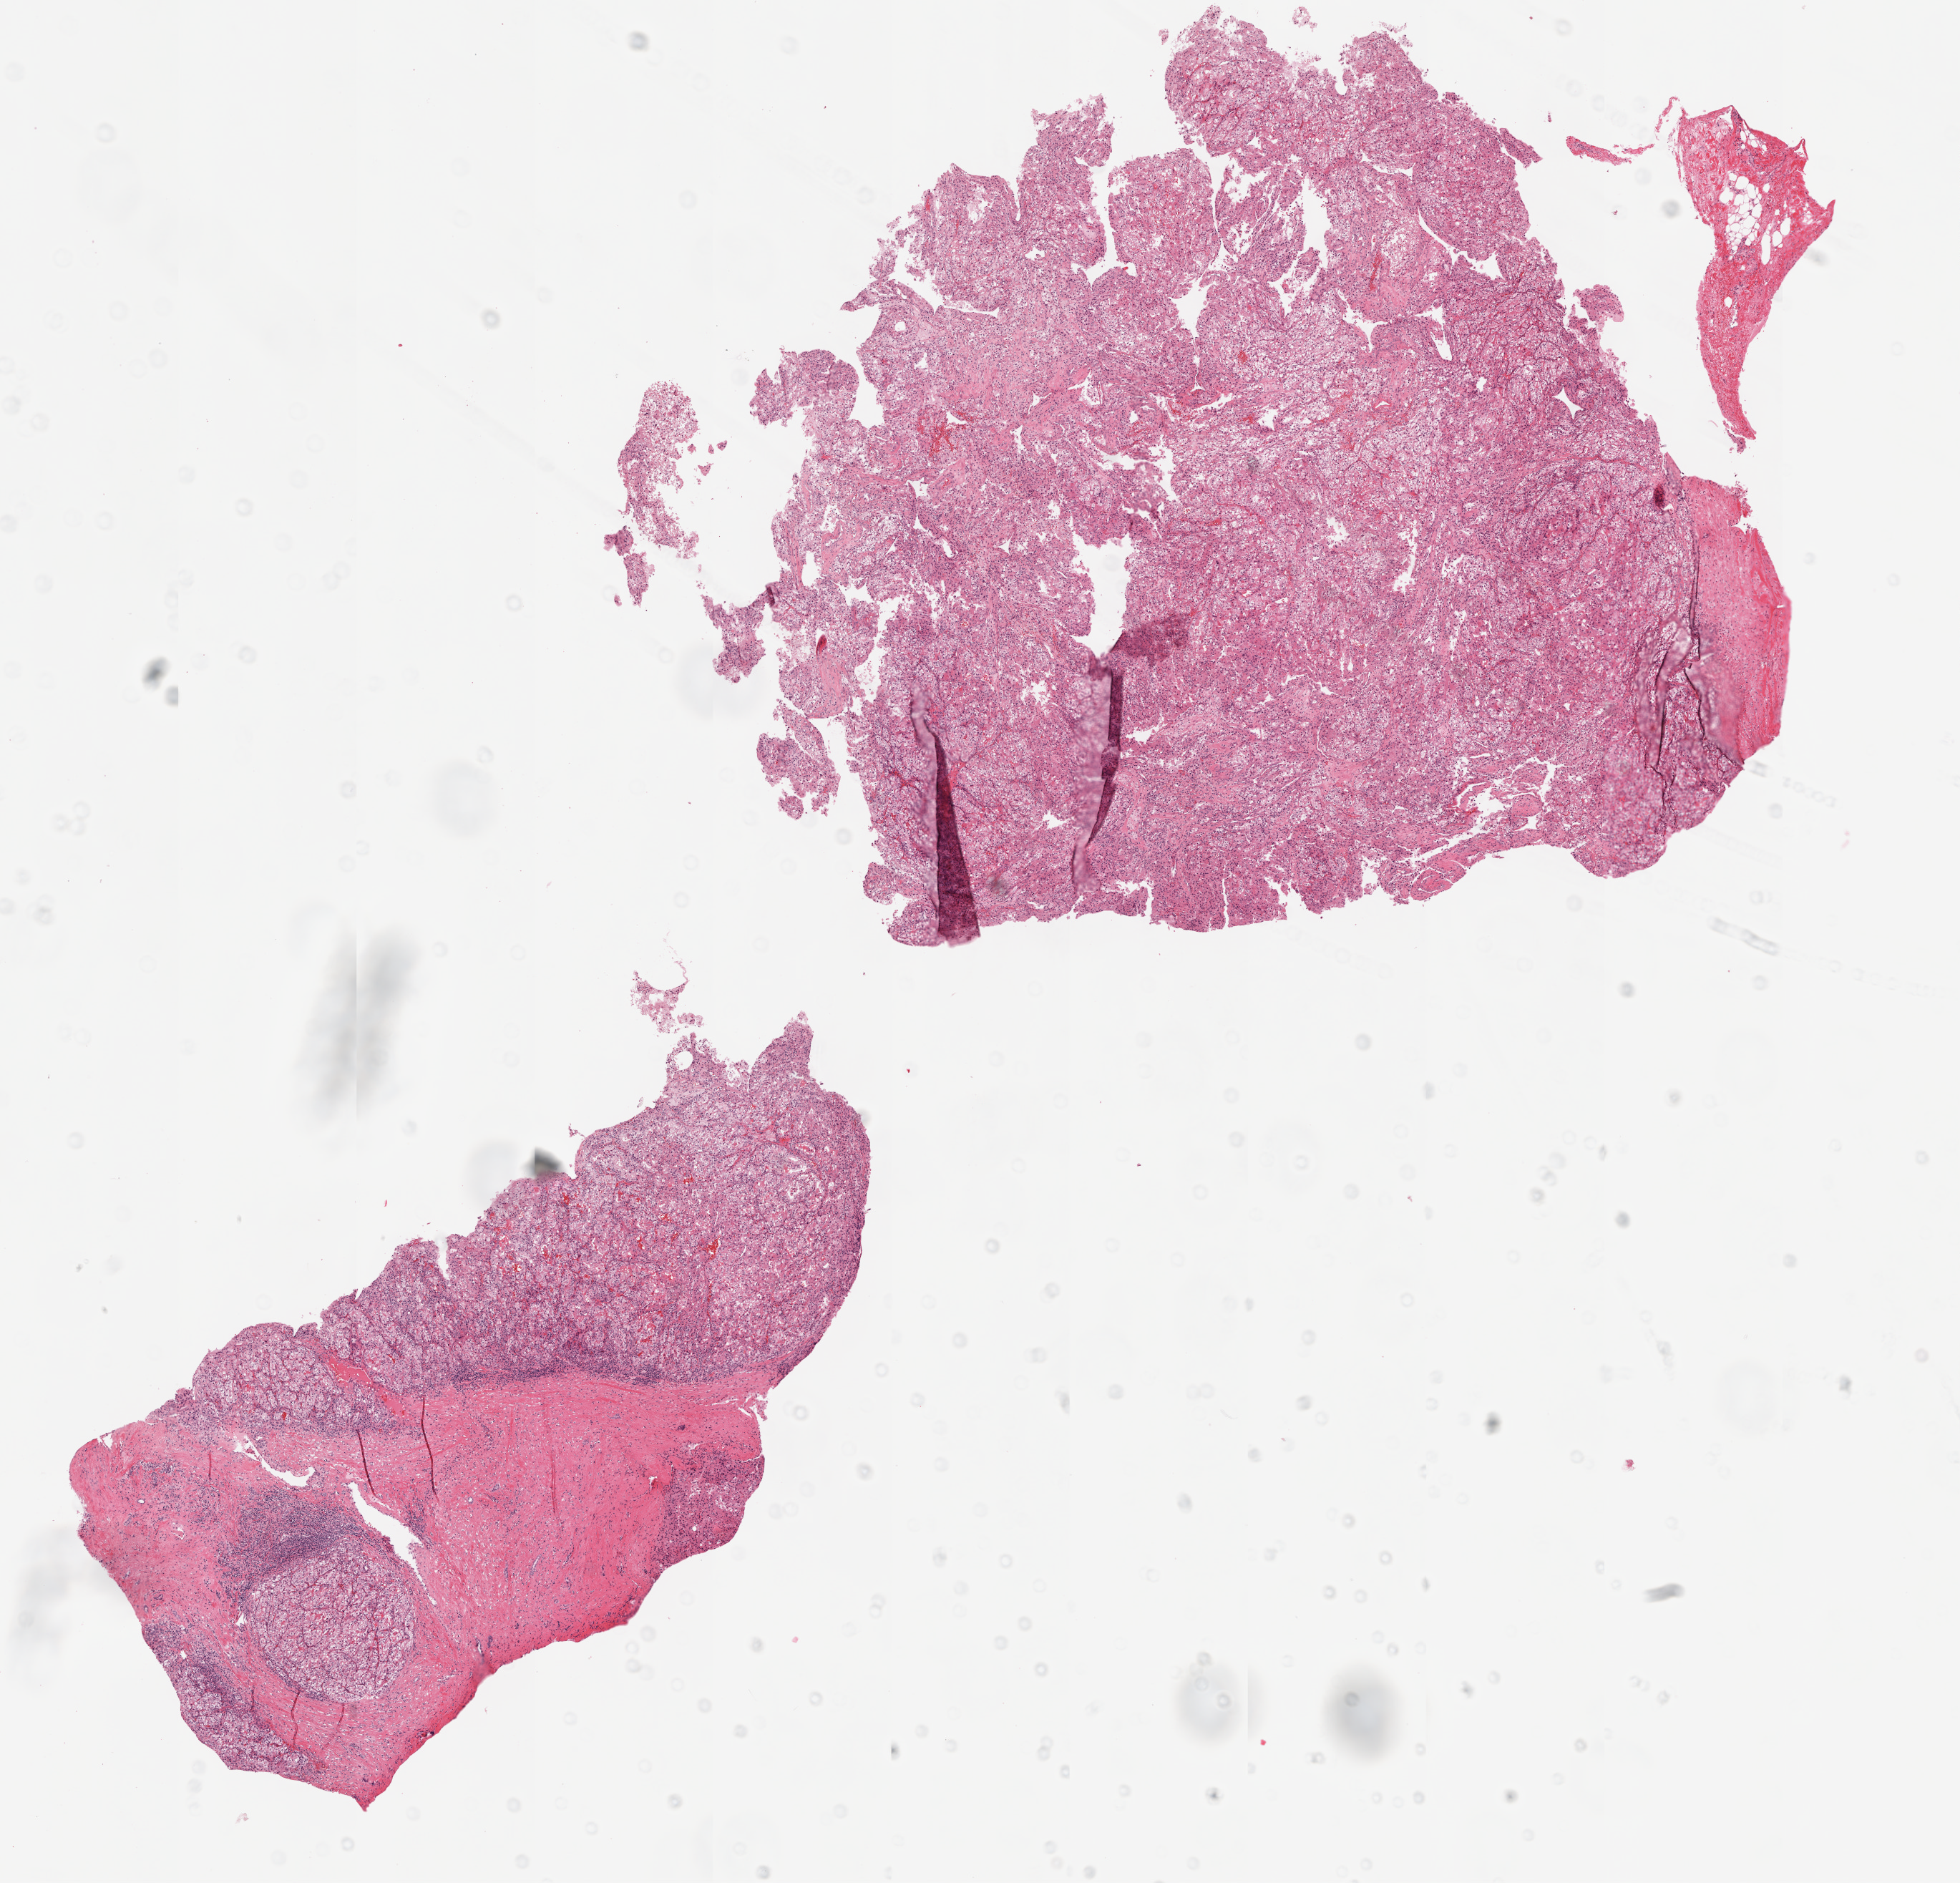
Whole-slide histology image, H&E-stained, low-resolution overview of the scanned area, about 10.9 x 10.5 mm. Tumour tissue sample, sampled site: kidney. 41-year-old male patient. Histologic grade: G3 (poorly differentiated). Composition of this section per pathologist review: tumour nuclei 85%, necrosis 0%.
Histologic diagnosis: Renal cell carcinoma, NOS. AJCC pathologic stage: II. Primary tumour site (as recorded): upper pole.